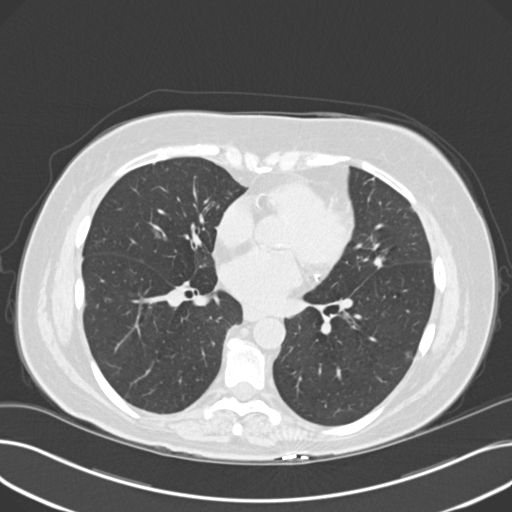
Chest CT (low-dose screening protocol), one axial image. Third annual screen. Lung window (W 1500 / L -600 HU). 2 mm slice thickness. 120 kVp. 512 × 512 image matrix. Female, age 60 years at enrolment.
• Lesion marked by an expert reader, box from (x=360, y=249) to (x=403, y=283) px.
• The screening reader recorded 8 non-calcified nodules or masses ≥4 mm on this exam (right upper lobe, lingula, lingula, right middle lobe, right lower lobe, left lower lobe, left lower lobe, left lower lobe); which of them this box marks is not recorded.
• Later outcome: lung cancer diagnosed 176 days after this screen — non-small cell carcinoma, left upper lobe, poorly differentiated (G3), stage IB (AJCC 6th edition), 7 mm at pathology.